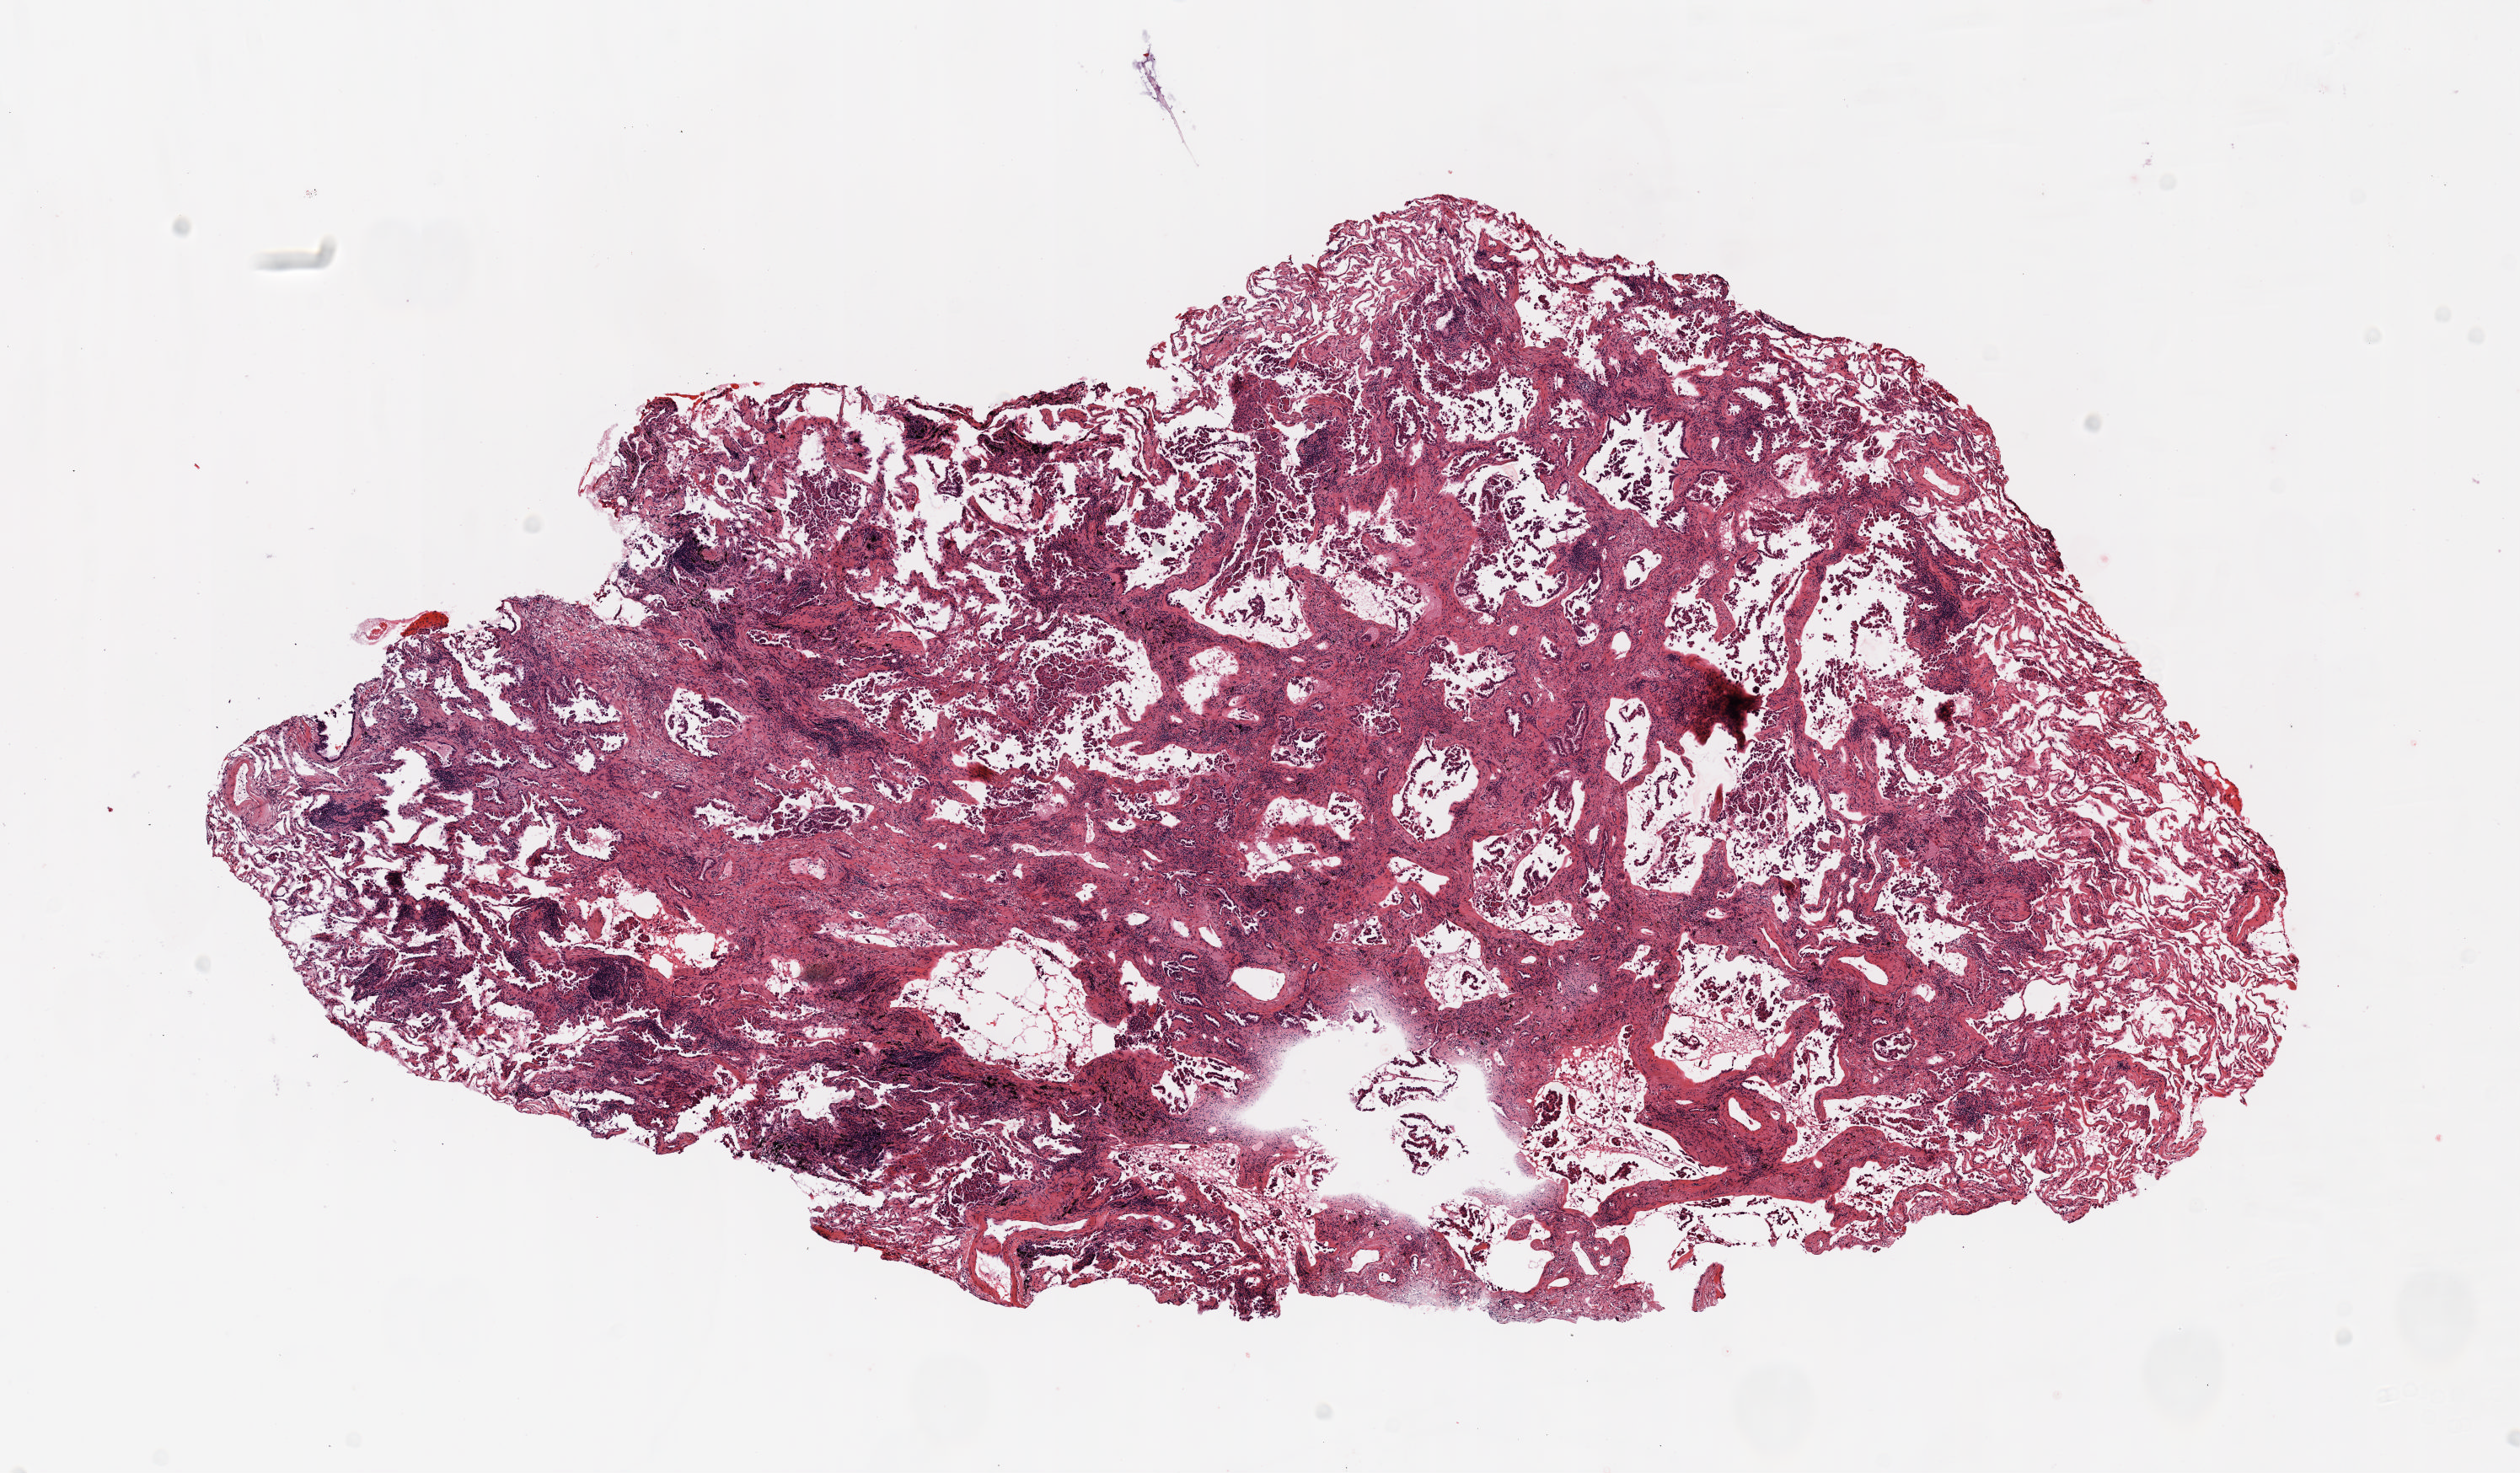
Whole-slide histology image, Hematoxylin and eosin (H&E) stained — a low-resolution overview of the entire scanned area, about 12.0 x 7.0 mm; FFPE section; lung. Female, age 72 at enrolment. Former smoker at enrolment. Grade: well differentiated (G1).
Primary tumour location (clinical record): right upper lobe. Stage (AJCC 6th edition): IA. Tumour size (pathology): 8 mm. ICD-O-3 topography: upper lobe of lung (C34.1). Participant's lung-cancer diagnosis: Bronchiolo-alveolar adenocarcinoma, NOS.